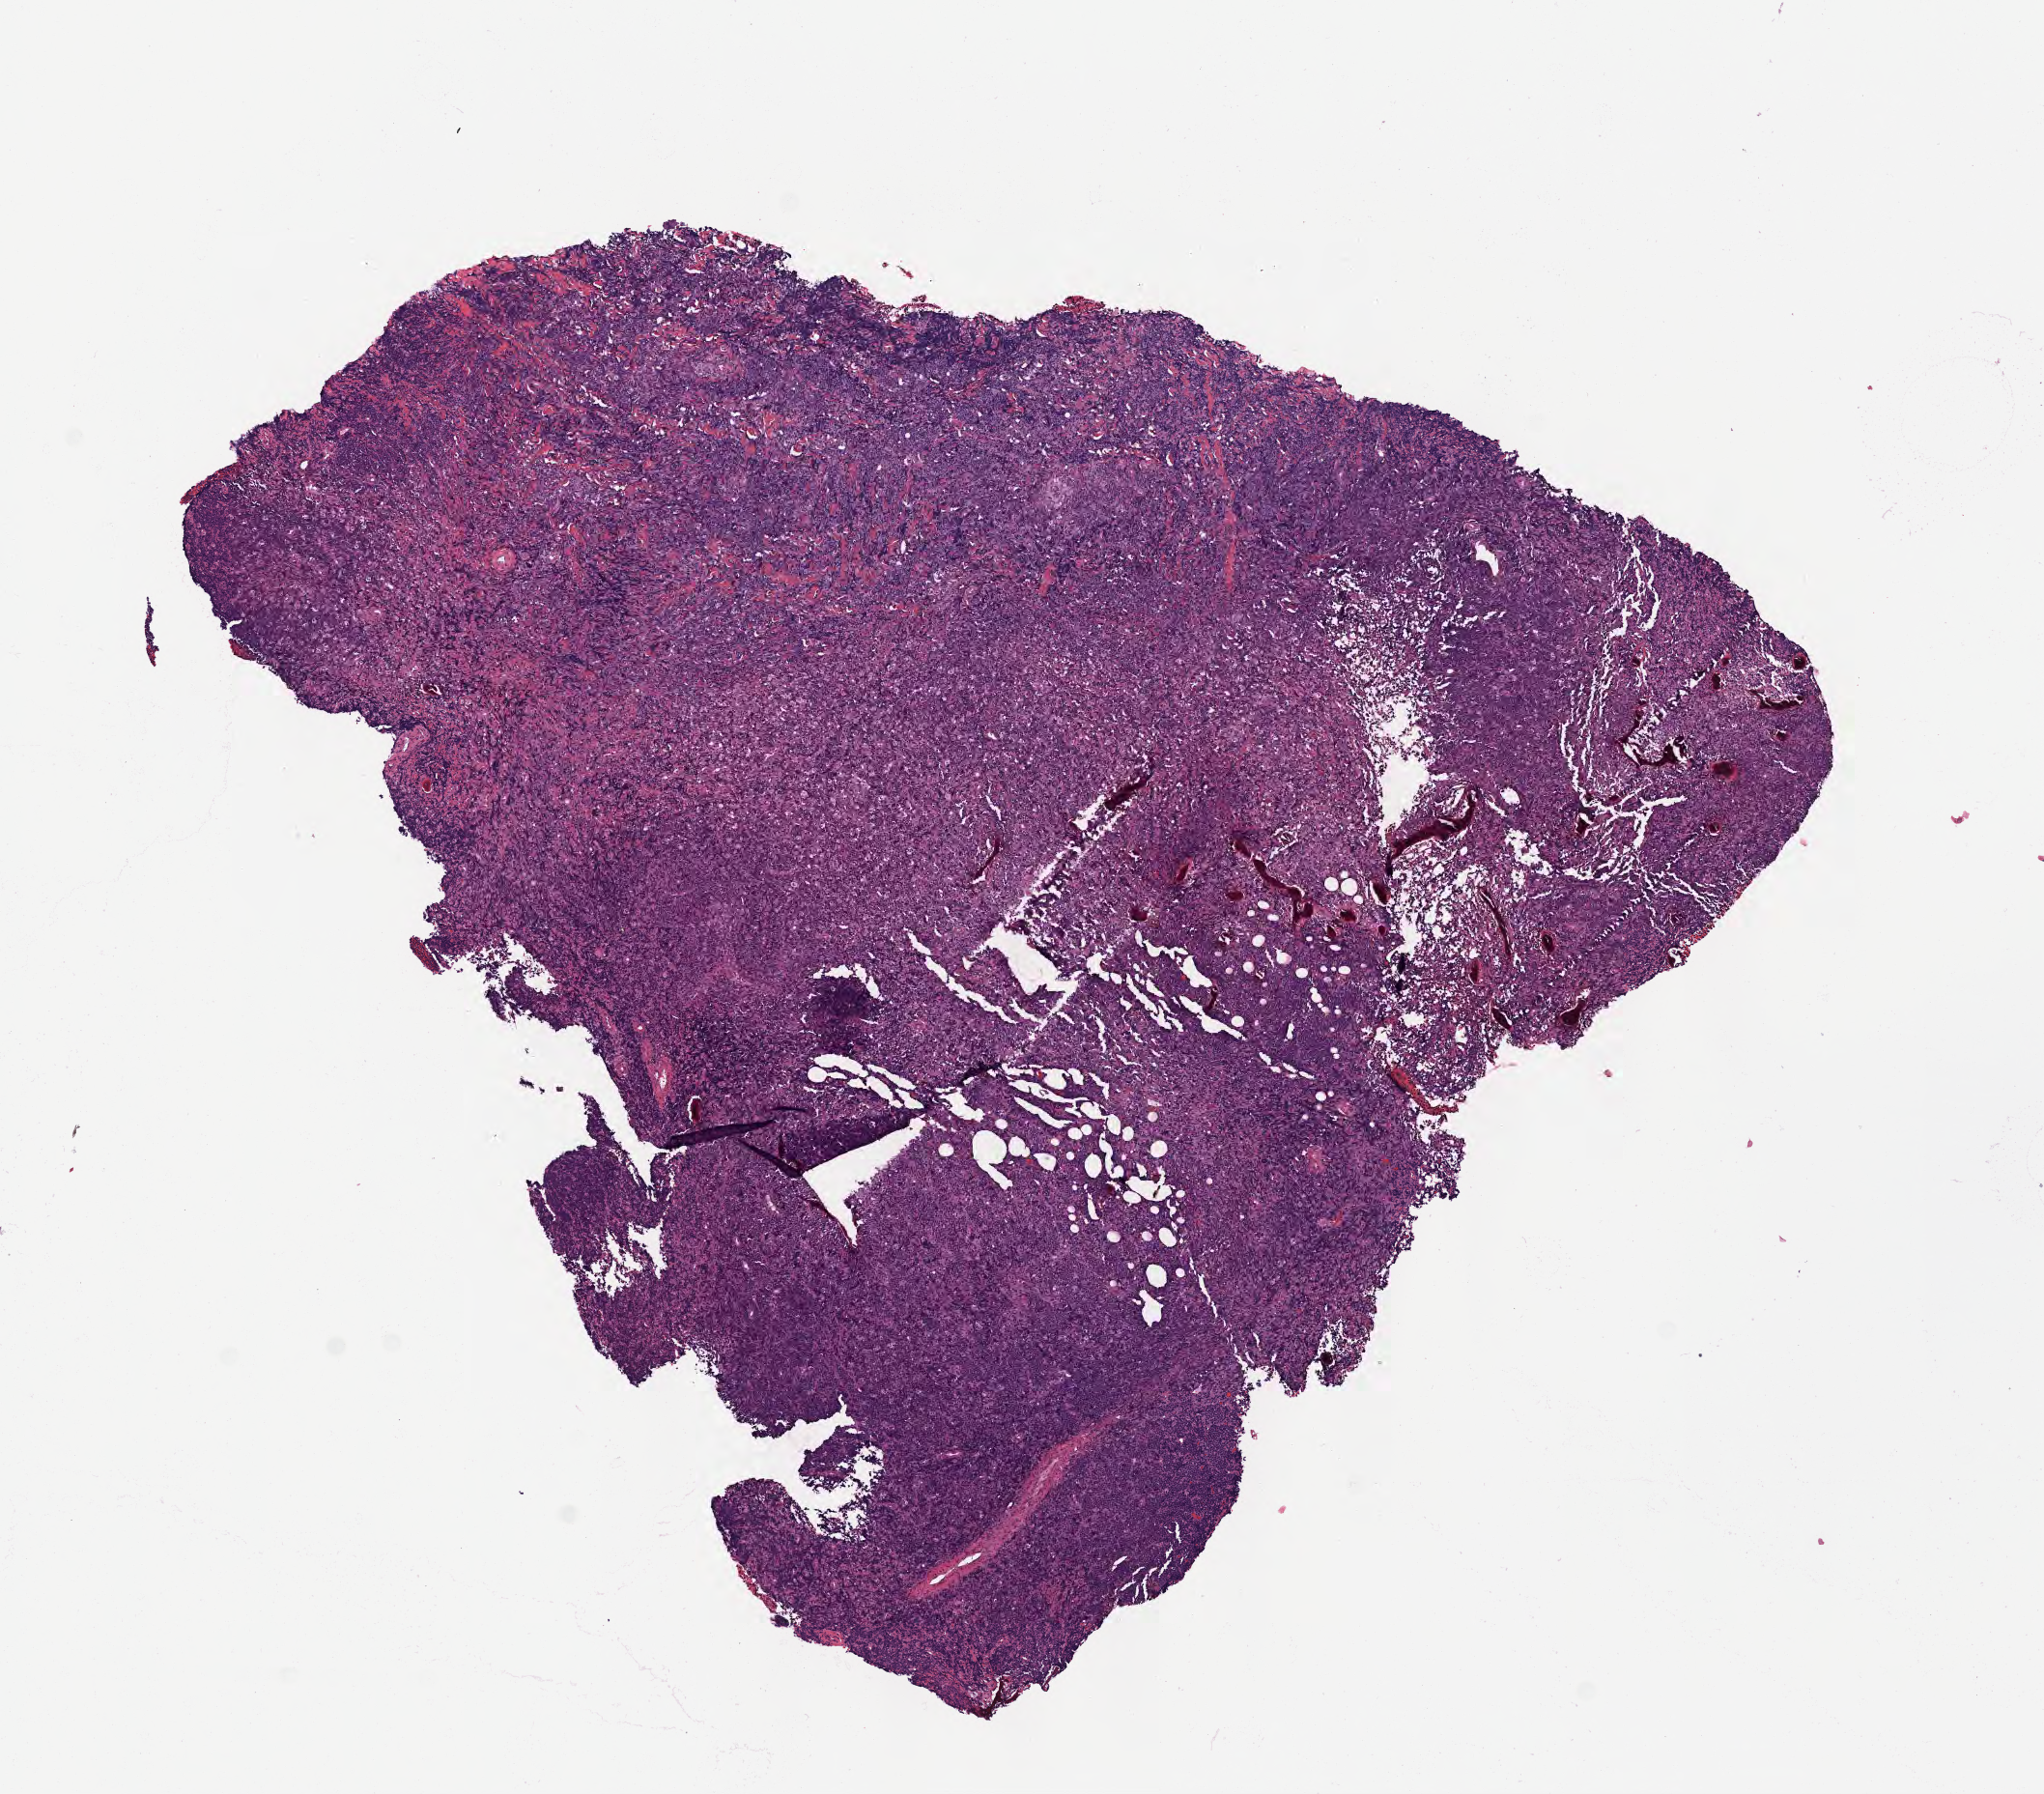
Digitized hematoxylin and eosin (H&E)-stained section, low-resolution overview of the scanned area, about 8.6 x 7.5 mm. Formalin-fixed, paraffin-embedded (FFPE) tissue. Specimen: primary tumor. Site: vestibule of mouth. Male patient; age at initial diagnosis 5 years. Pathologist review of this section (percent, as recorded): tumor cells 95%, tumor nuclei 95%, stromal cells 3%, necrosis 2%, normal cells 0%. Infiltration values recorded for this section: lymphocyte infiltration 40%, monocyte infiltration 30%, neutrophil infiltration 5%.
Diagnosis: Diffuse large B-cell lymphoma, NOS. Ann Arbor stage (patient): Stage IV. Section: top of the tissue portion.